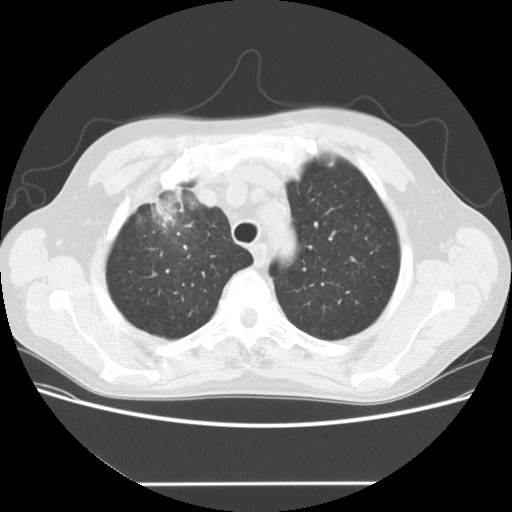
Low-dose screening chest CT, axial slice, baseline screening round, lung window (W 1500 / L -600 HU), 2.5 mm slice thickness, standard (soft-tissue) reconstruction kernel (STANDARD), slice 29 of 153 in the series. Male, age 56 years at enrolment. Current smoker at enrolment.
Expert-annotated lung lesion, bounding box <128,176,208,241> (left, top, right, bottom; pixels). The screening reader recorded 2 non-calcified nodules or masses ≥4 mm on this exam; which of them this box marks is not recorded. Official screen result: positive, change unspecified: nodule(s) >= 4 mm or enlarging nodule(s), mass(es), or other non-specific abnormalities suspicious for lung cancer.